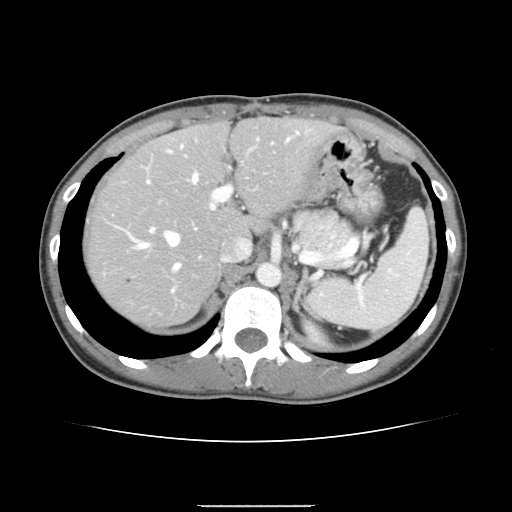
Contrast-enhanced abdominal CT, one axial slice; position 105 of 150 along the scan axis; intravenous contrast given; soft-tissue window (W 400 / L 40 HU); 2.5 mm slice thickness; 512 × 512 image matrix. Female patient, age 32 years. Case-level facts recorded for this patient, not image findings: diagnosis: colorectal cancer liver metastases, imaged before liver resection.
Outlined on this slice (manually delineated by an expert):
- hepatic veins: bounding box (x1, y1, x2, y2) in pixels: (135, 174, 198, 270)
- liver: (88, 120, 334, 327)
- planned liver remnant (the part of the liver to remain after resection): (88, 120, 333, 281)
- portal vein (with intrahepatic branches): (129, 132, 300, 292)
- liver metastasis: (126, 278, 134, 285)